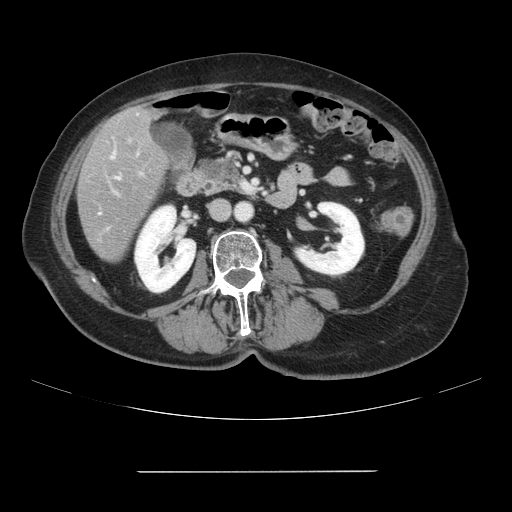
Contrast-enhanced abdominal CT, one axial slice. Slice 25 of 111 in the series (ordered by position). 120 kVp. Intravenous contrast given. Soft-tissue window (W 400 / L 40 HU). 2.5 mm slice thickness. 512 × 512 image matrix, field of view 400 × 400 mm. Female patient, age 74 years. From the clinical record (not read from this slice): diagnosis: colorectal cancer liver metastases, imaged before liver resection; multiple liver metastases: yes; largest metastasis: 1.1 cm; disease in both lobes: yes.
Annotated regions visible in this slice (expert manual segmentation):
- liver: bounding box <78,107,168,262> (left, top, right, bottom; pixels)
- planned liver remnant (the part of the liver to remain after resection): <145,111,150,116>